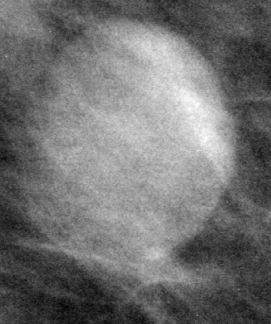
Cropped region of a digitized screen-film mammogram centred on a radiologist-marked abnormality; left breast; MLO view.
Marked abnormality: mass, shape oval, margins circumscribed; BI-RADS assessment category 3; pathology (as recorded): benign.